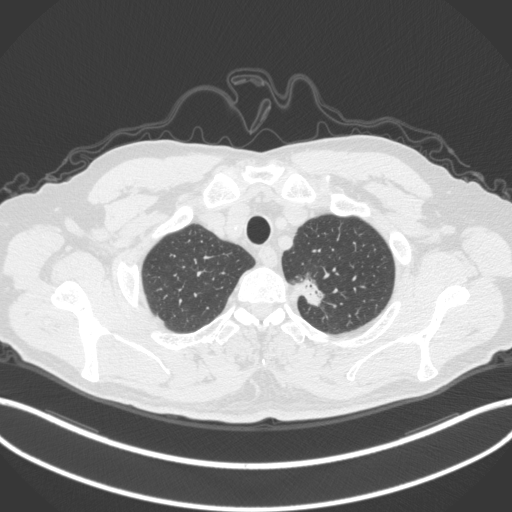
Chest CT, one axial slice. Reconstruction kernel B31f. 120 kVp. Lung window (W 1500 / L -600 HU). 1 mm slice thickness. 512 × 512 image matrix, field of view 400 × 400 mm. Male patient, age 64 years. Case-level facts recorded for this patient, not image findings: clinical TNM (as recorded): T1c N0 M0.
Outlined on this slice (rectangle marked by the reading radiologist):
- lung tumour (recorded histology: adenocarcinoma): bounding box [x1, y1, x2, y2] px = [298, 271, 330, 314]